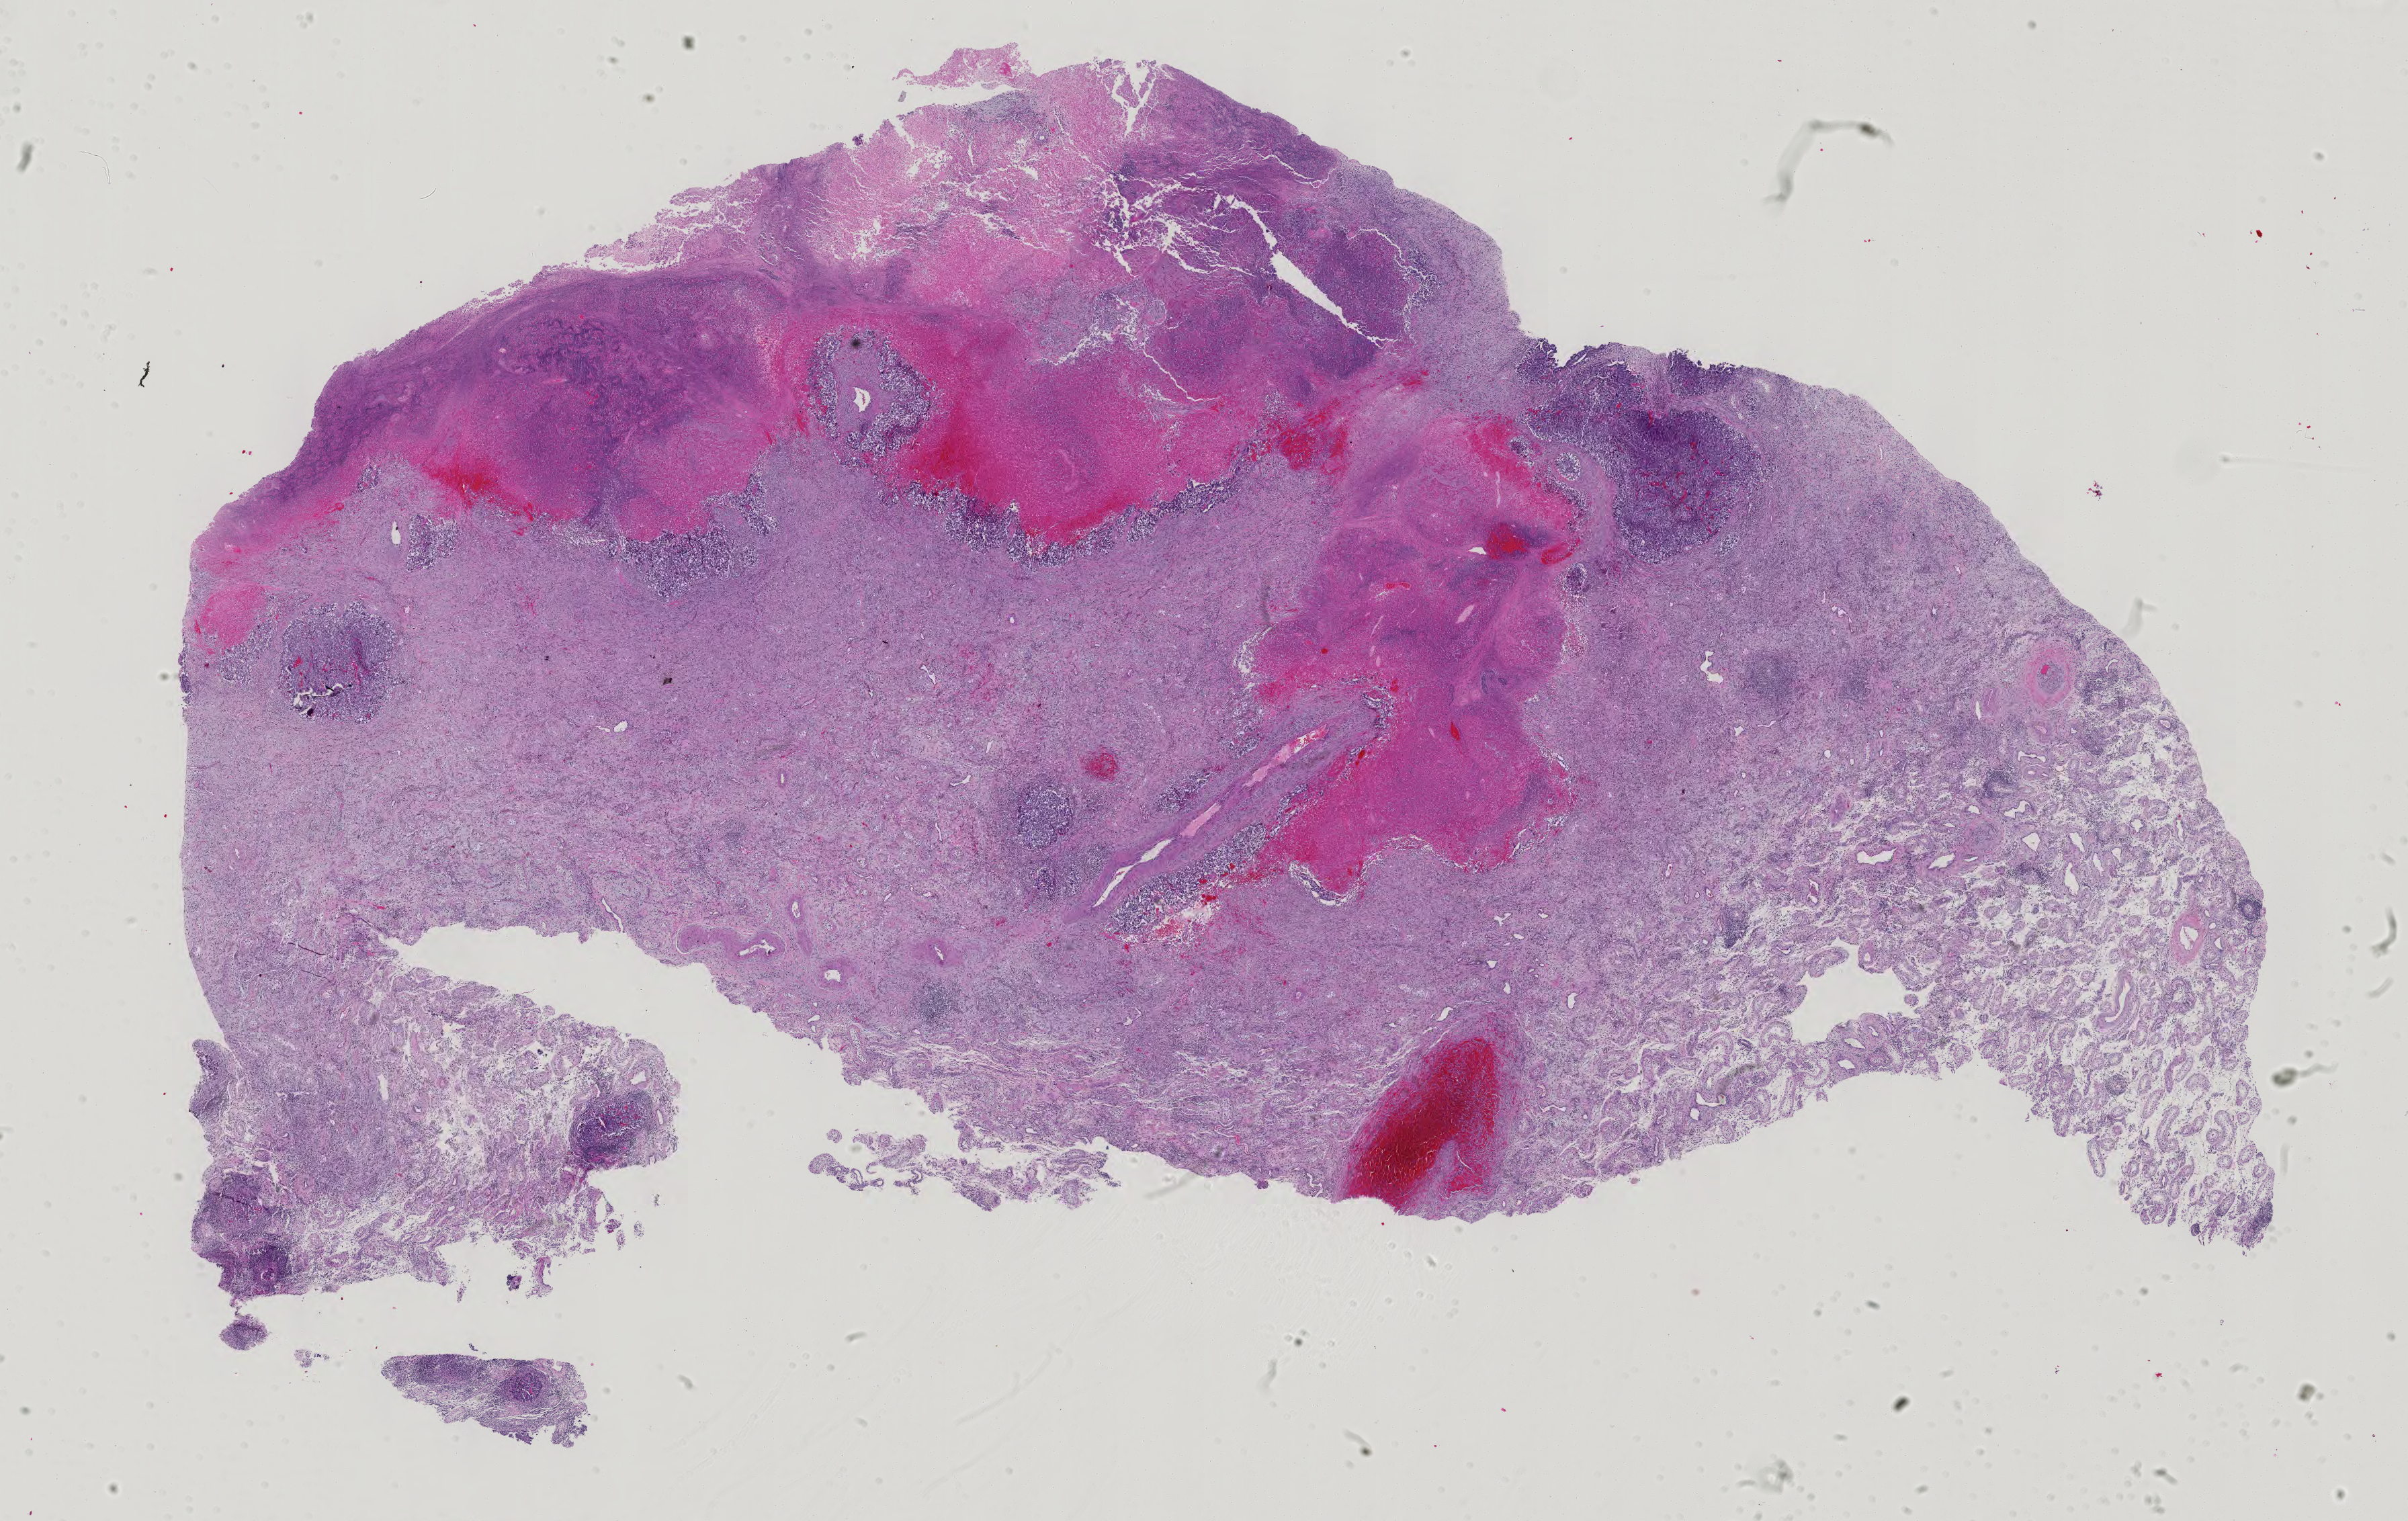
Whole-slide histology image, H&E, shown as a low-resolution overview of the whole scanned area (about 26.1 x 16.5 mm, slide scanned at 40x). FFPE section. Sample: primary tumour, testis. Patient: male, age at initial diagnosis 31 years.
Histologic diagnosis: Embryonal carcinoma, NOS.